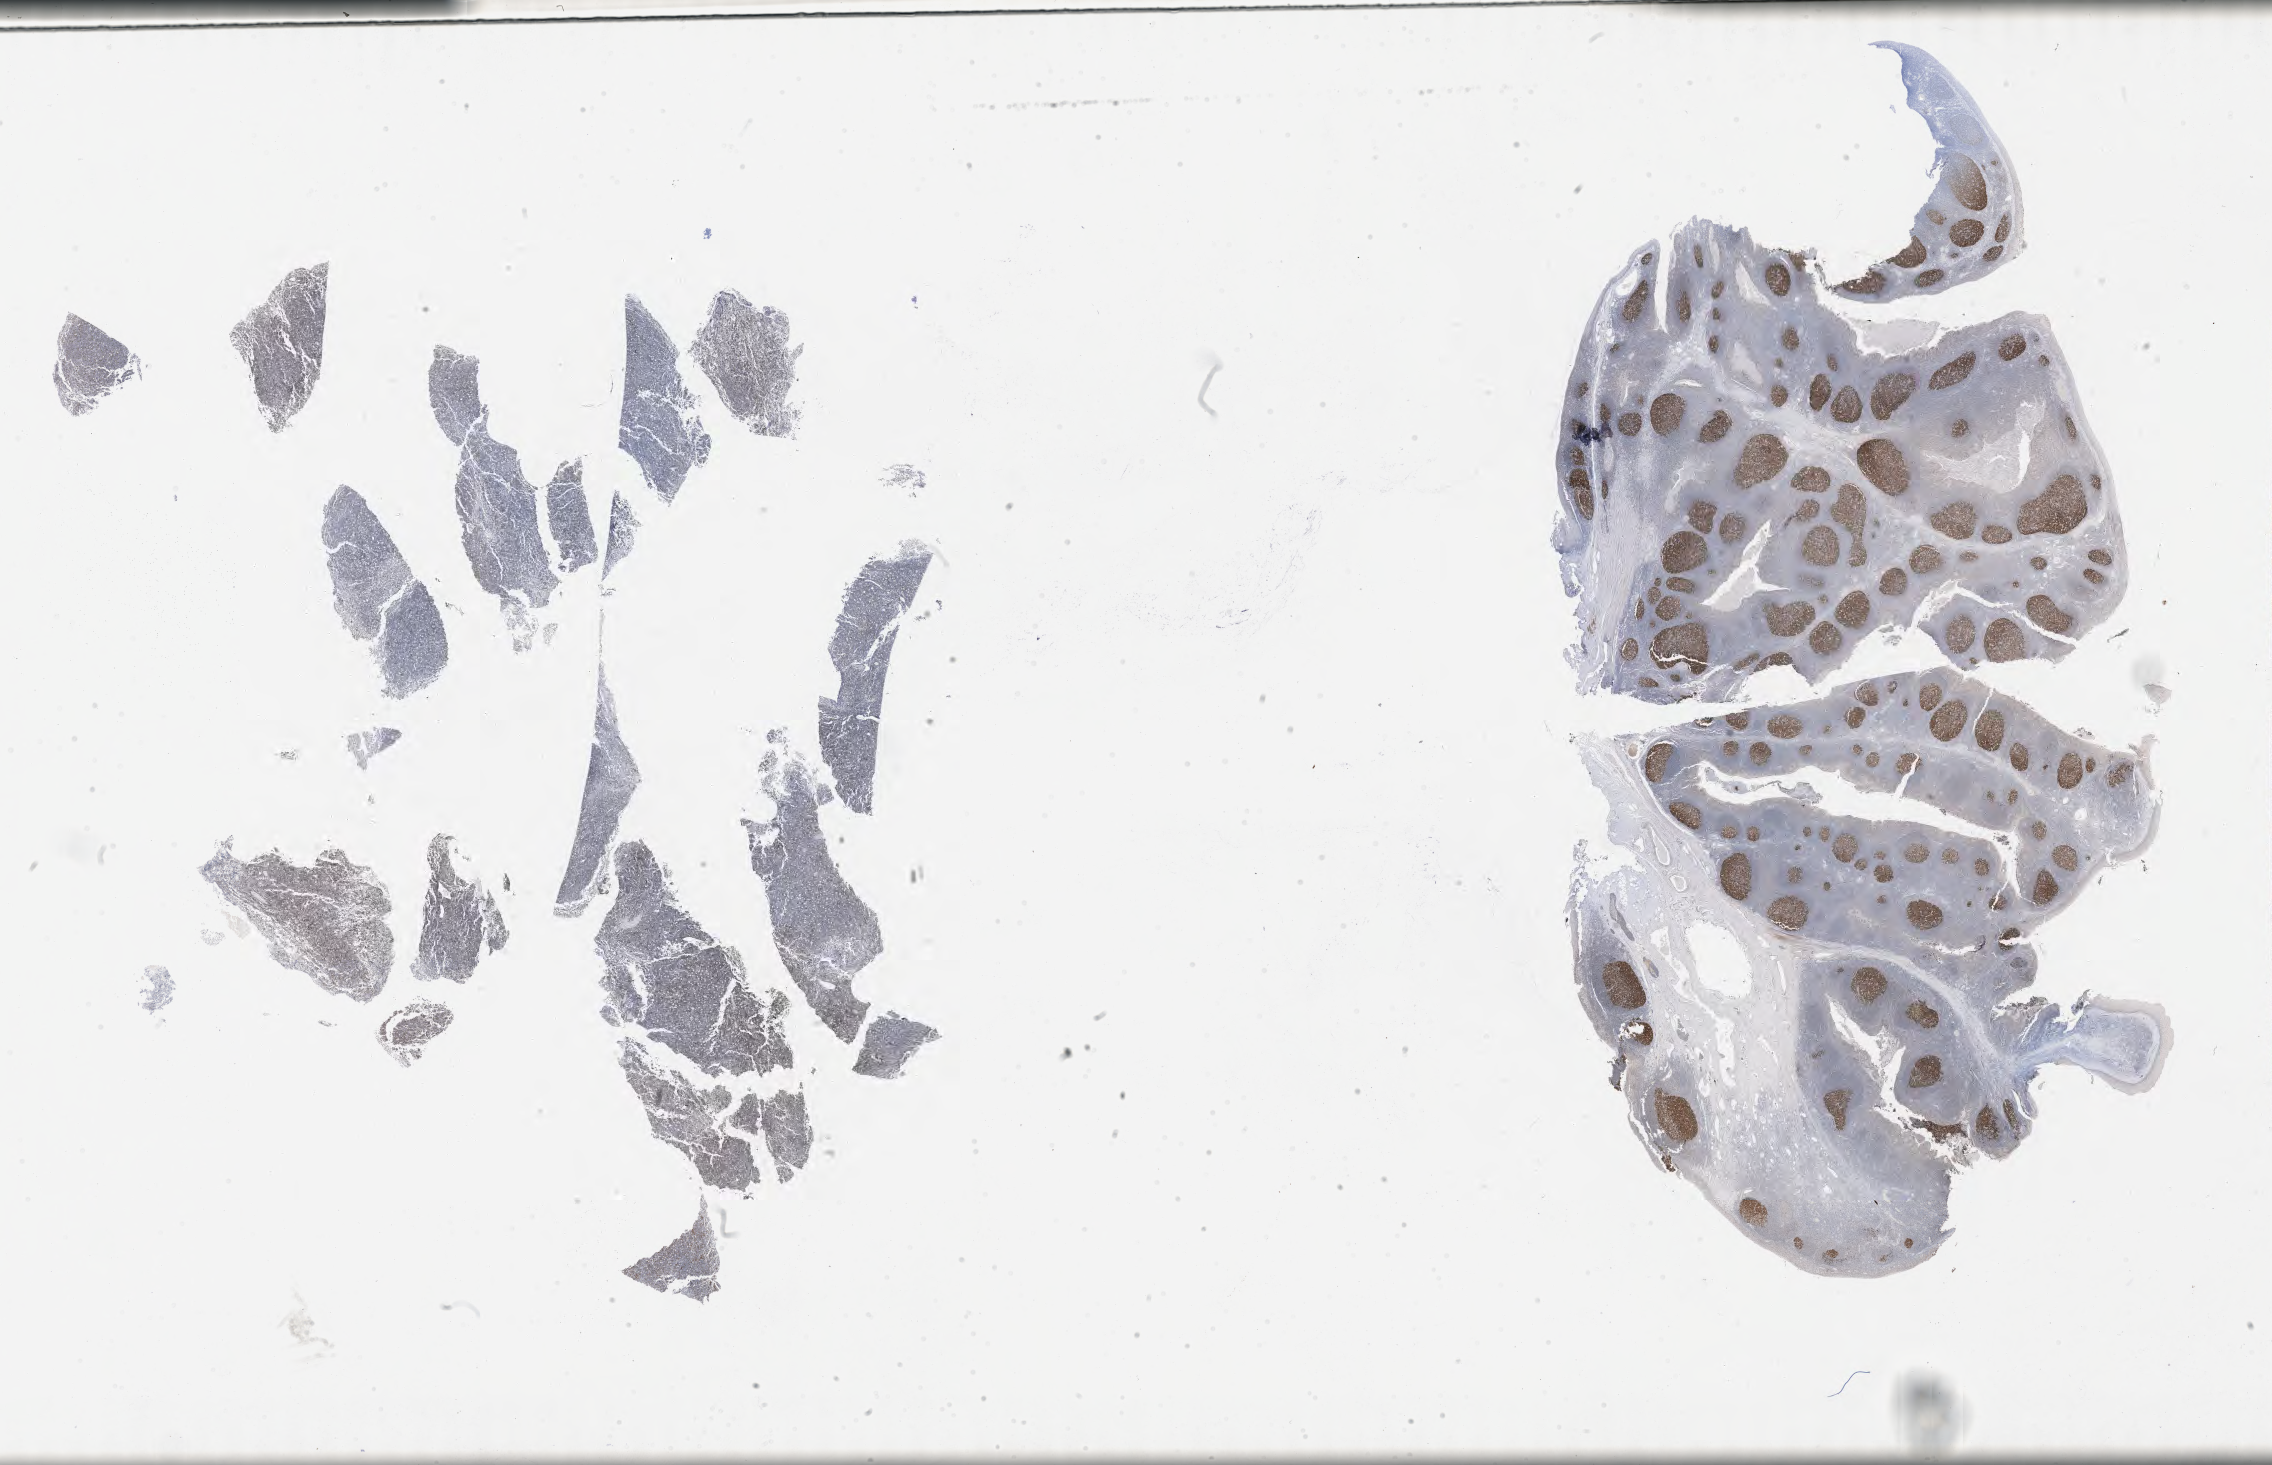
Whole-slide image, immunohistochemical stain for BCL6, shown as a low-resolution overview of the whole scanned area (about 36.7 x 23.7 mm). Tumor tissue. Patient male; age 11 years.
• histologic diagnosis: Burkitt lymphoma, NOS